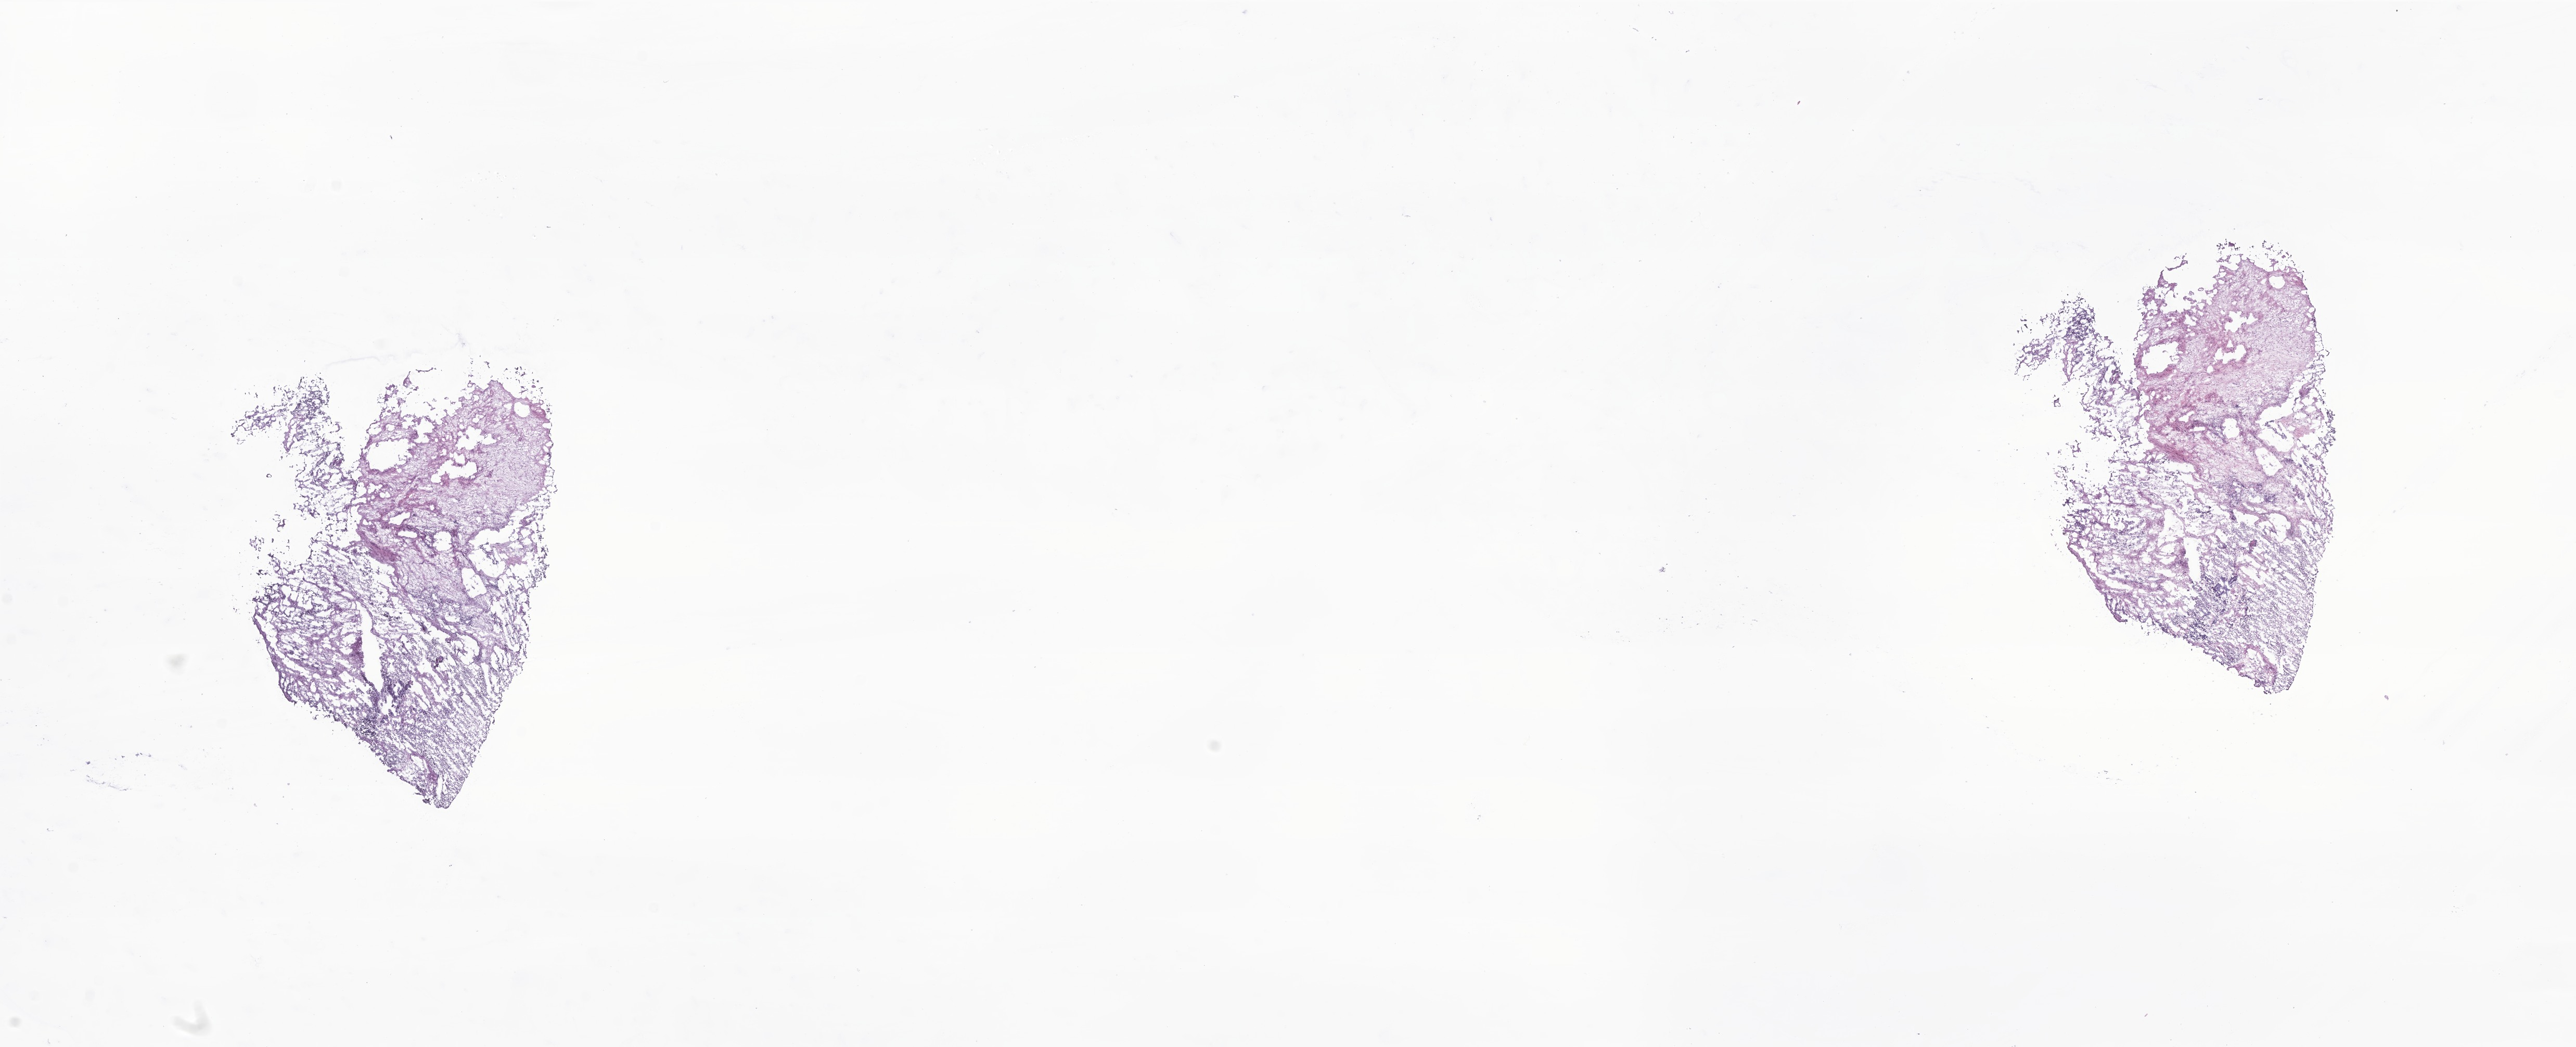
Digitized haematoxylin and eosin-stained section of tumor tissue from the adrenal gland — whole scanned area (about 20.9 x 8.5 mm) shown as a low-resolution overview; frozen section (OCT-embedded). Patient: female, age 694 days (about 1.9 years).
• recorded diagnosis: Neuroblastoma, NOS